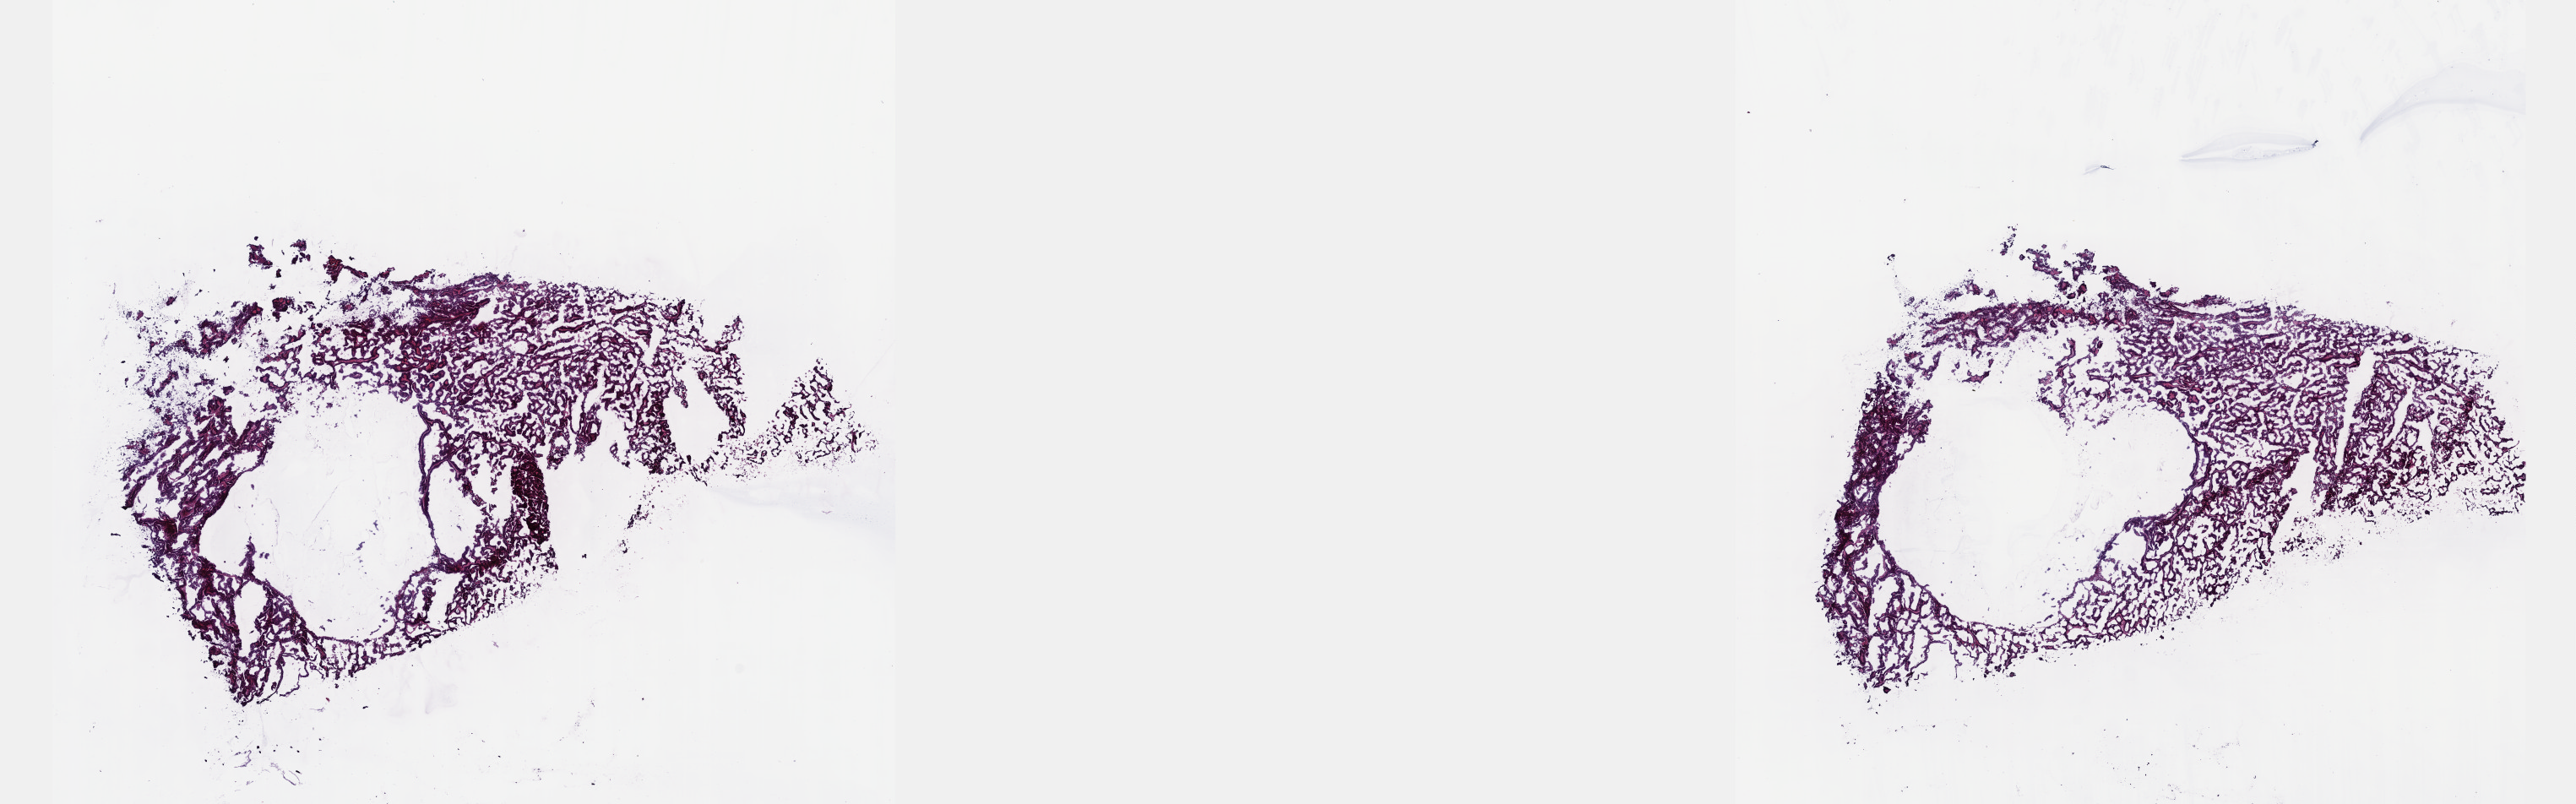
H&E whole-slide image, low-resolution overview of the scanned area, about 24.6 x 7.7 mm. Frozen section from the top of the tissue portion. Kidney, primary tumour sample. Male, age 58 years at initial diagnosis.
Histologic diagnosis: Papillary adenocarcinoma, NOS.